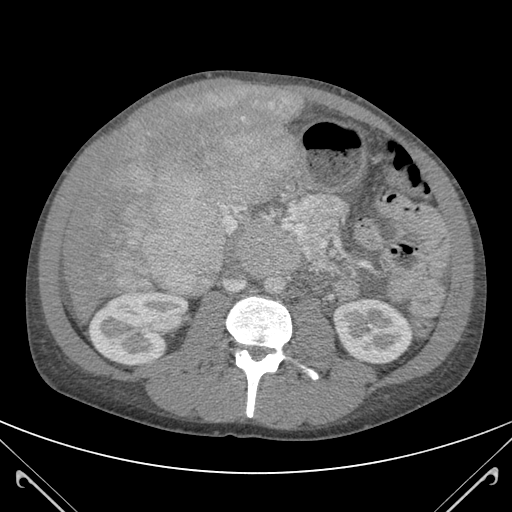
Contrast-enhanced abdominal CT (liver protocol), one axial slice. Slice 48 of 118 in the series (ordered by position). 120 kVp. Soft-tissue window (W 400 / L 40 HU). 3 mm slice thickness. 512 × 512 image matrix. From the clinical record (not read from this slice): diagnosis: hepatocellular carcinoma (patient treated with transarterial chemoembolisation; whether this scan precedes or follows treatment is not stated here); TNM stage (as recorded): Stage-IIIB; Child-Pugh class: A.
Annotated regions visible in this slice (semi-automatic segmentation, software-assisted and operator-edited):
- abdominal aorta: bounding box (x1, y1, x2, y2) in pixels: (266, 275, 285, 296)
- liver parenchyma outside the tumour (the mass and vessels are separate outlines, so this box may not span the whole liver): (61, 85, 299, 315)
- mass: (96, 85, 304, 295)